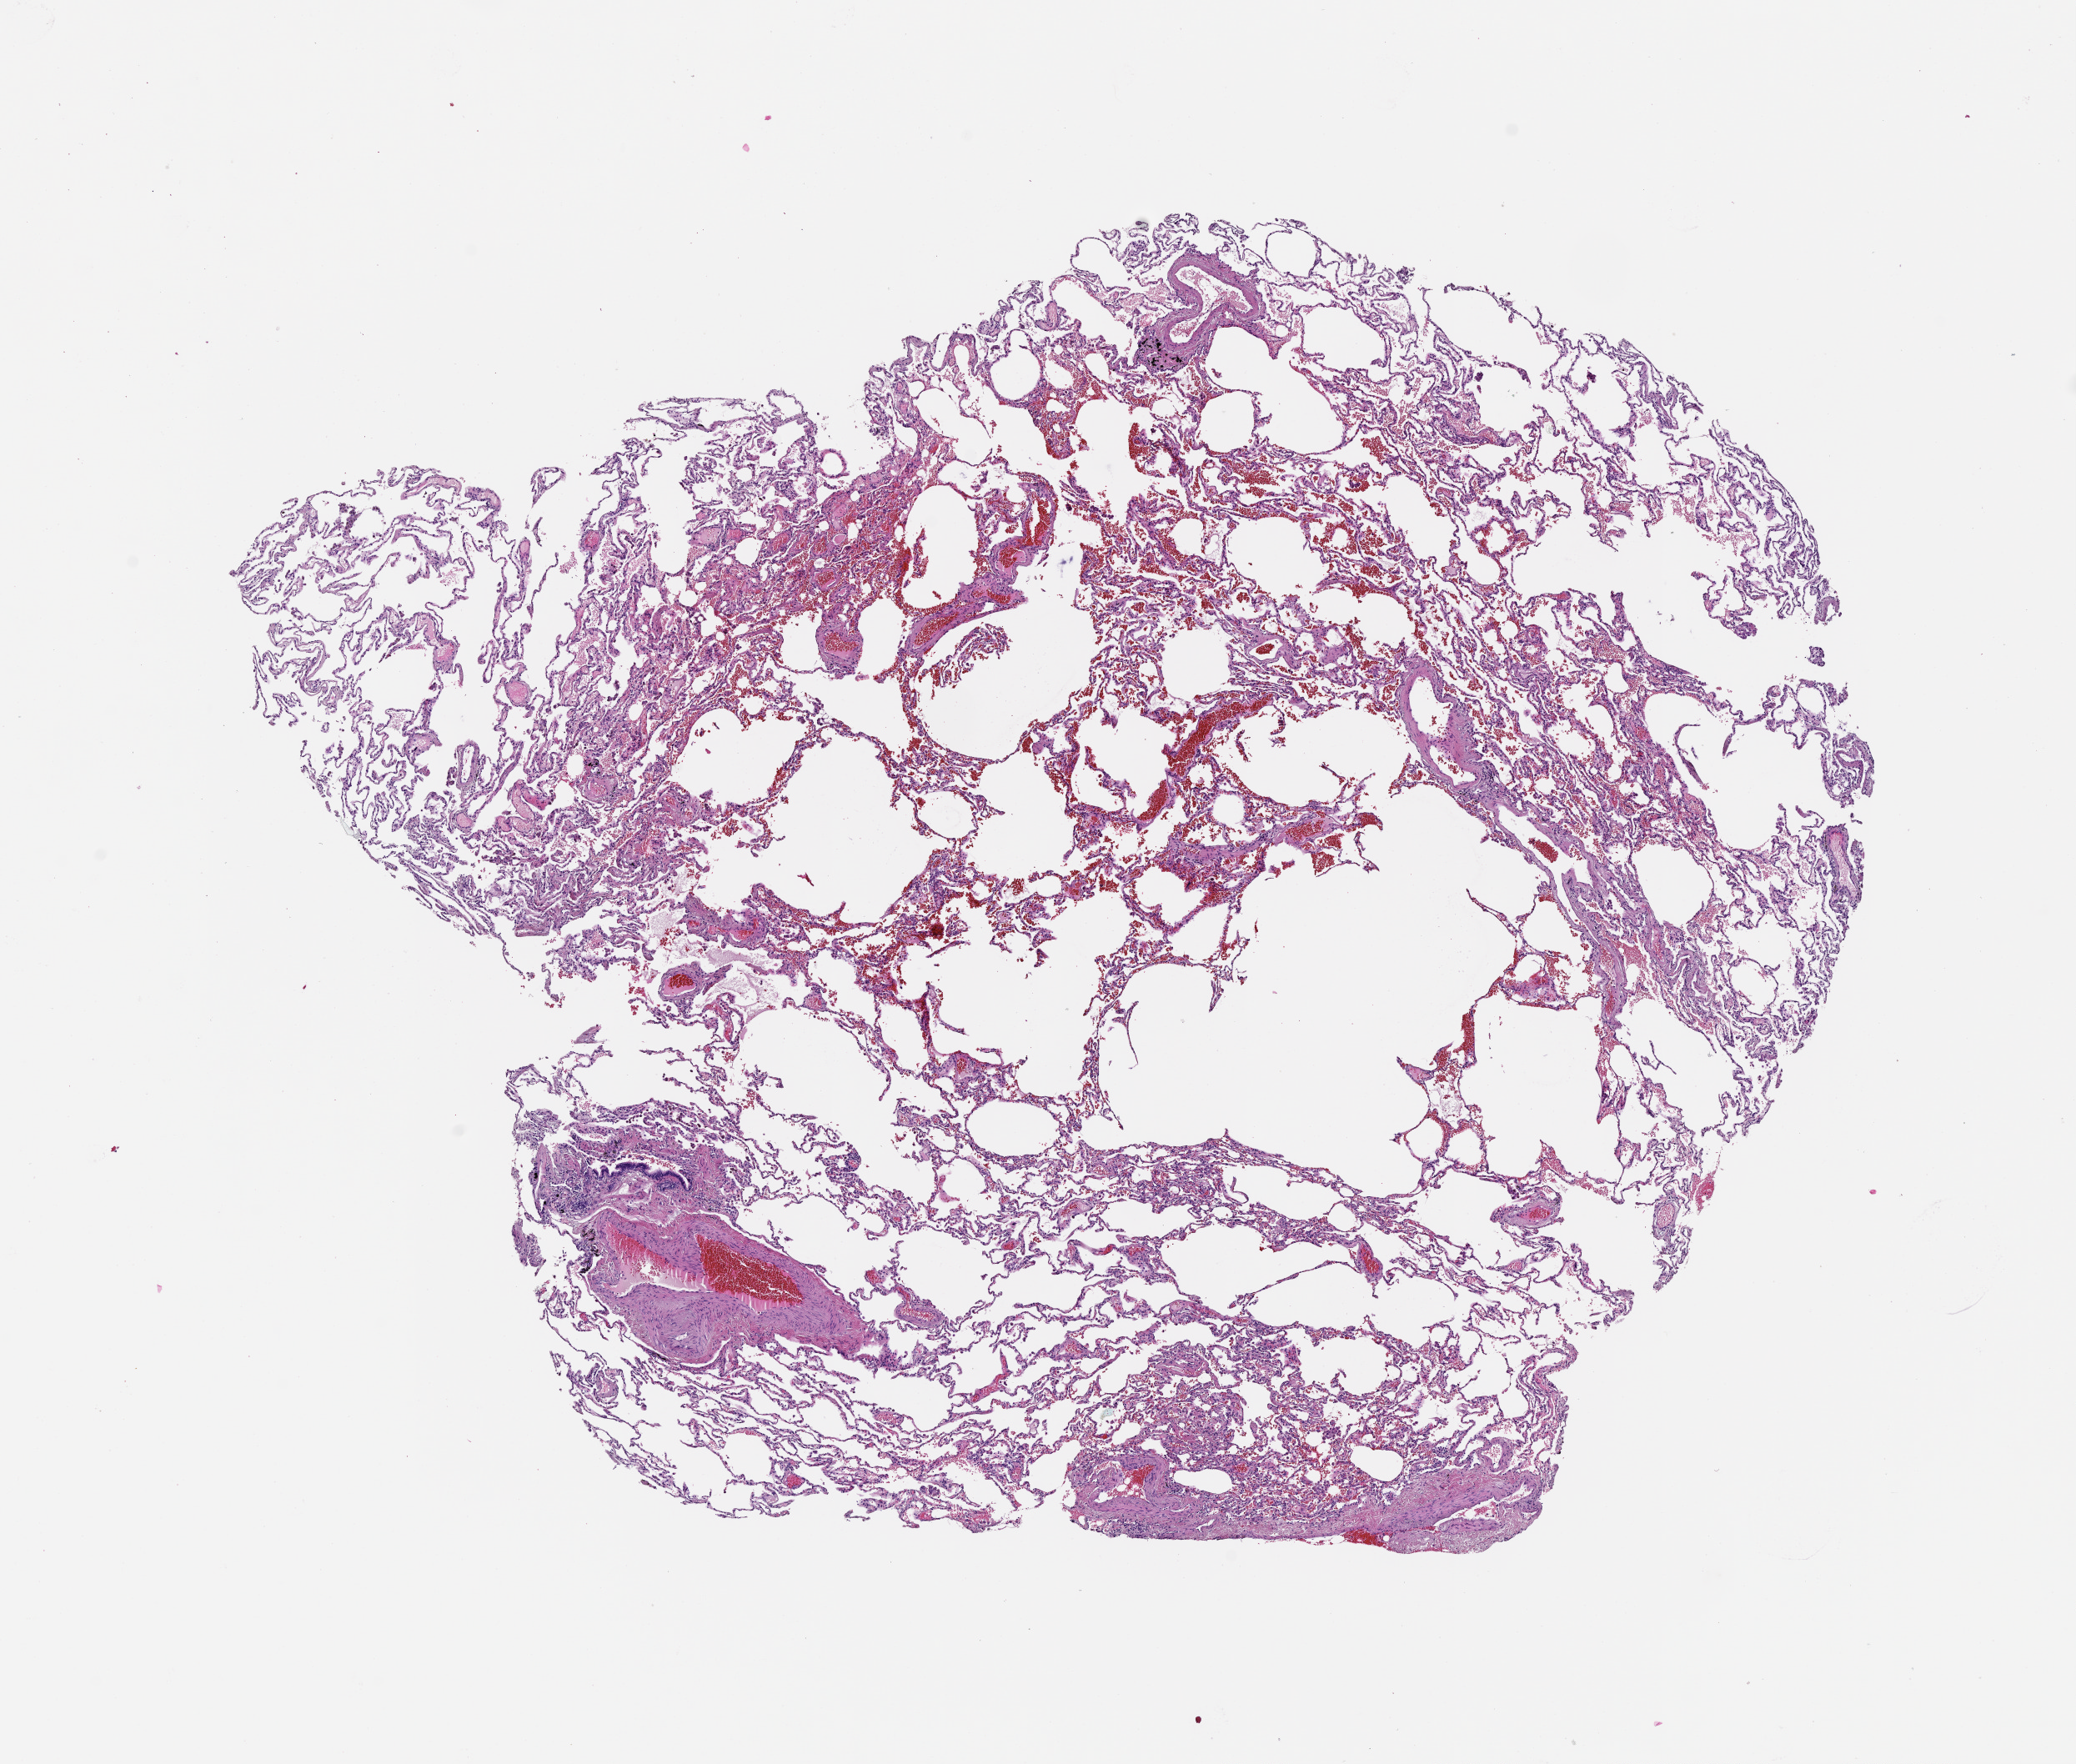
Whole-slide histology image, Hematoxylin and eosin (H&E) stained, low-resolution overview of the scanned area, about 10.0 x 8.5 mm (acquisition: 20x scan); lung, normal (non-tumour) tissue. Patient: male, age 67 years.
- this section: normal (non-tumour) tissue from the same patient
- patient diagnosis (cohort enrolment): squamous cell carcinoma (lung)